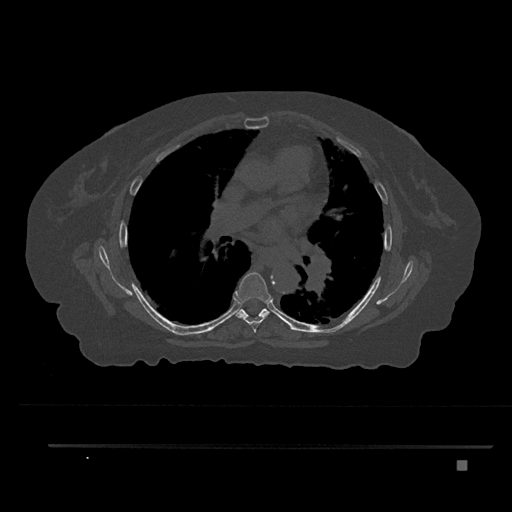
CT including the spine, one axial slice. Slice 512 of 797 in the series (ordered by position). Reconstruction kernel Br40s/3. Bone window (W 1800 / L 400 HU). 0.5 mm slice thickness. 512 × 512 image matrix. Patient: female, 76 years. From the clinical record (not read from this slice): primary cancer: lung.
Annotated regions visible in this slice (semi-automatically segmented with operator editing):
- T6 vertebra: box from (x=233, y=272) to (x=271, y=332) px
- T7 vertebra: (x=238, y=309)–(x=270, y=318)